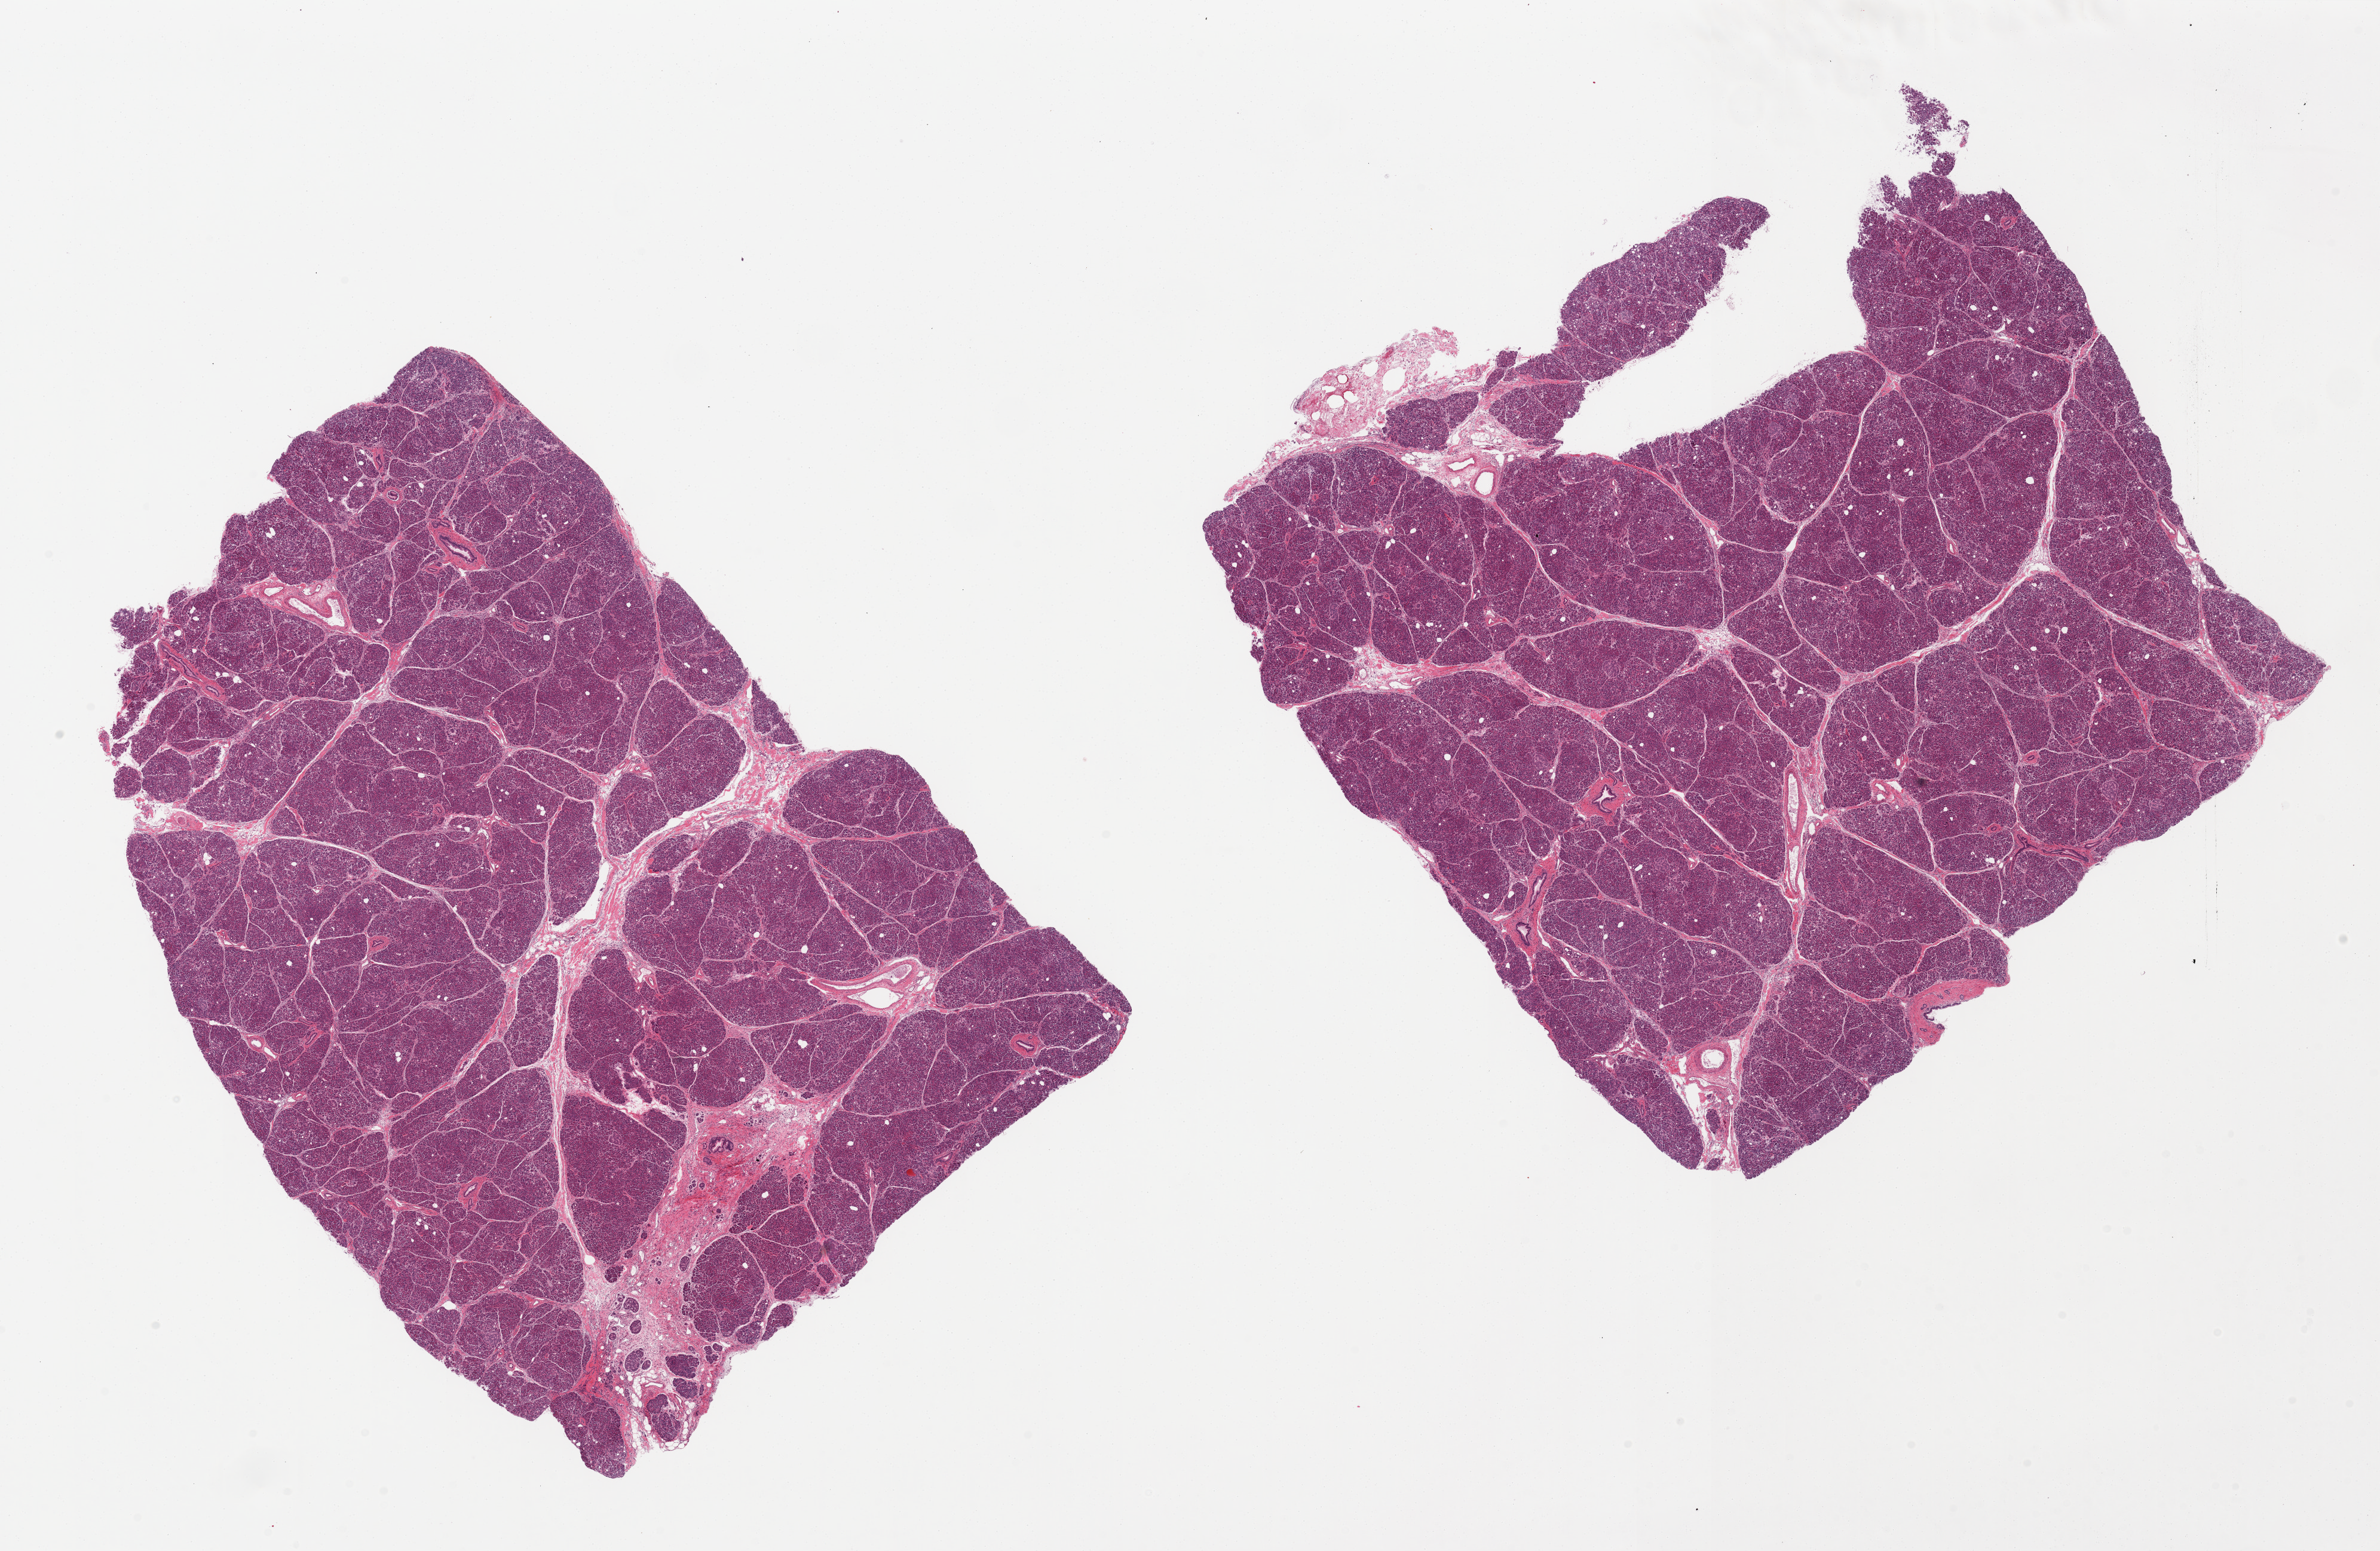
Whole-slide image, H&E stain — whole scanned area (about 31.5 x 20.5 mm, slide scanned at 20x) shown as a low-resolution overview. PAXgene-fixed paraffin-embedded (PFPE) section. Target tissue: pancreas. Donor tissue sample. Male donor.
Reviewer comment on this tissue sample: 2 pieces, 13.5x10 & 12x10mm.